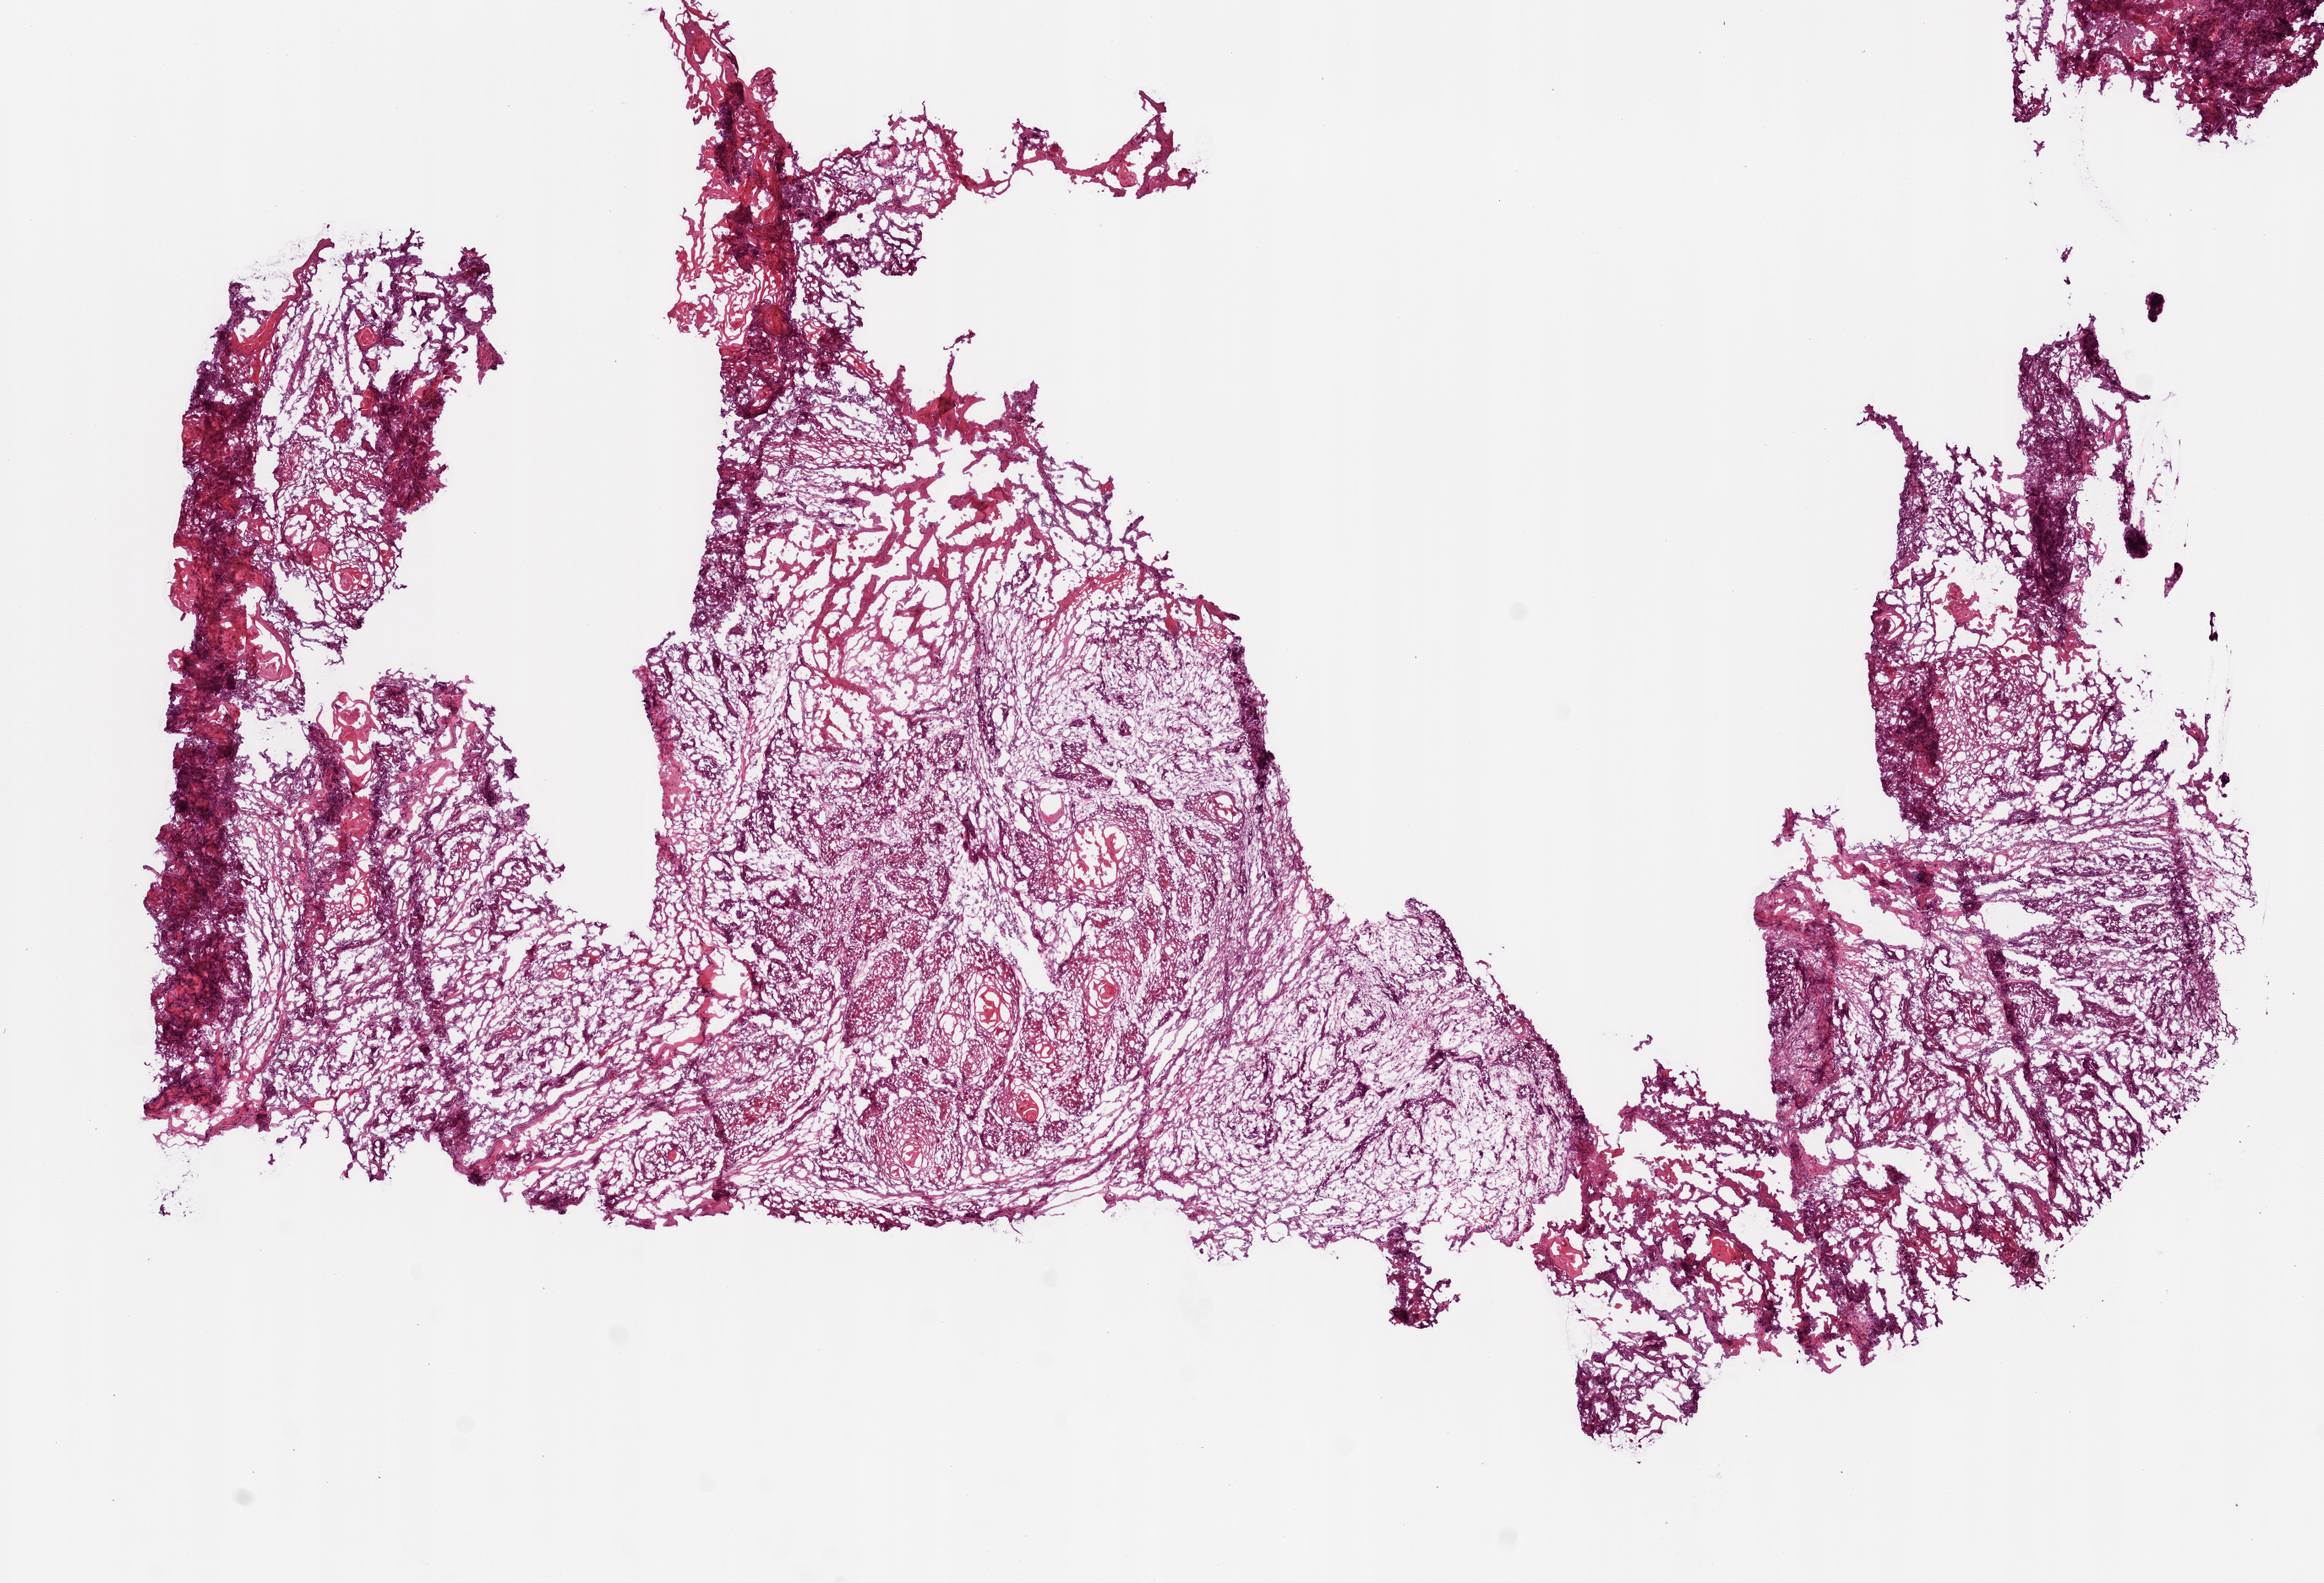
Whole-slide histology image, H&E, a low-resolution overview of the entire scanned area, about 11.0 x 7.5 mm. Frozen section from the top of the tissue portion. Head and neck, primary tumour sample. Male patient; age at initial diagnosis 51 years. Histologic grade: G2 (moderately differentiated). Pathologist review of this section (percent, as recorded): tumour cells 65%, tumour nuclei 80%, normal cells 0%, stromal cells 30%, necrosis 5%.
AJCC pathologic stage: IVA (6th edition). Histologic diagnosis: Squamous cell carcinoma, NOS (larynx, NOS).